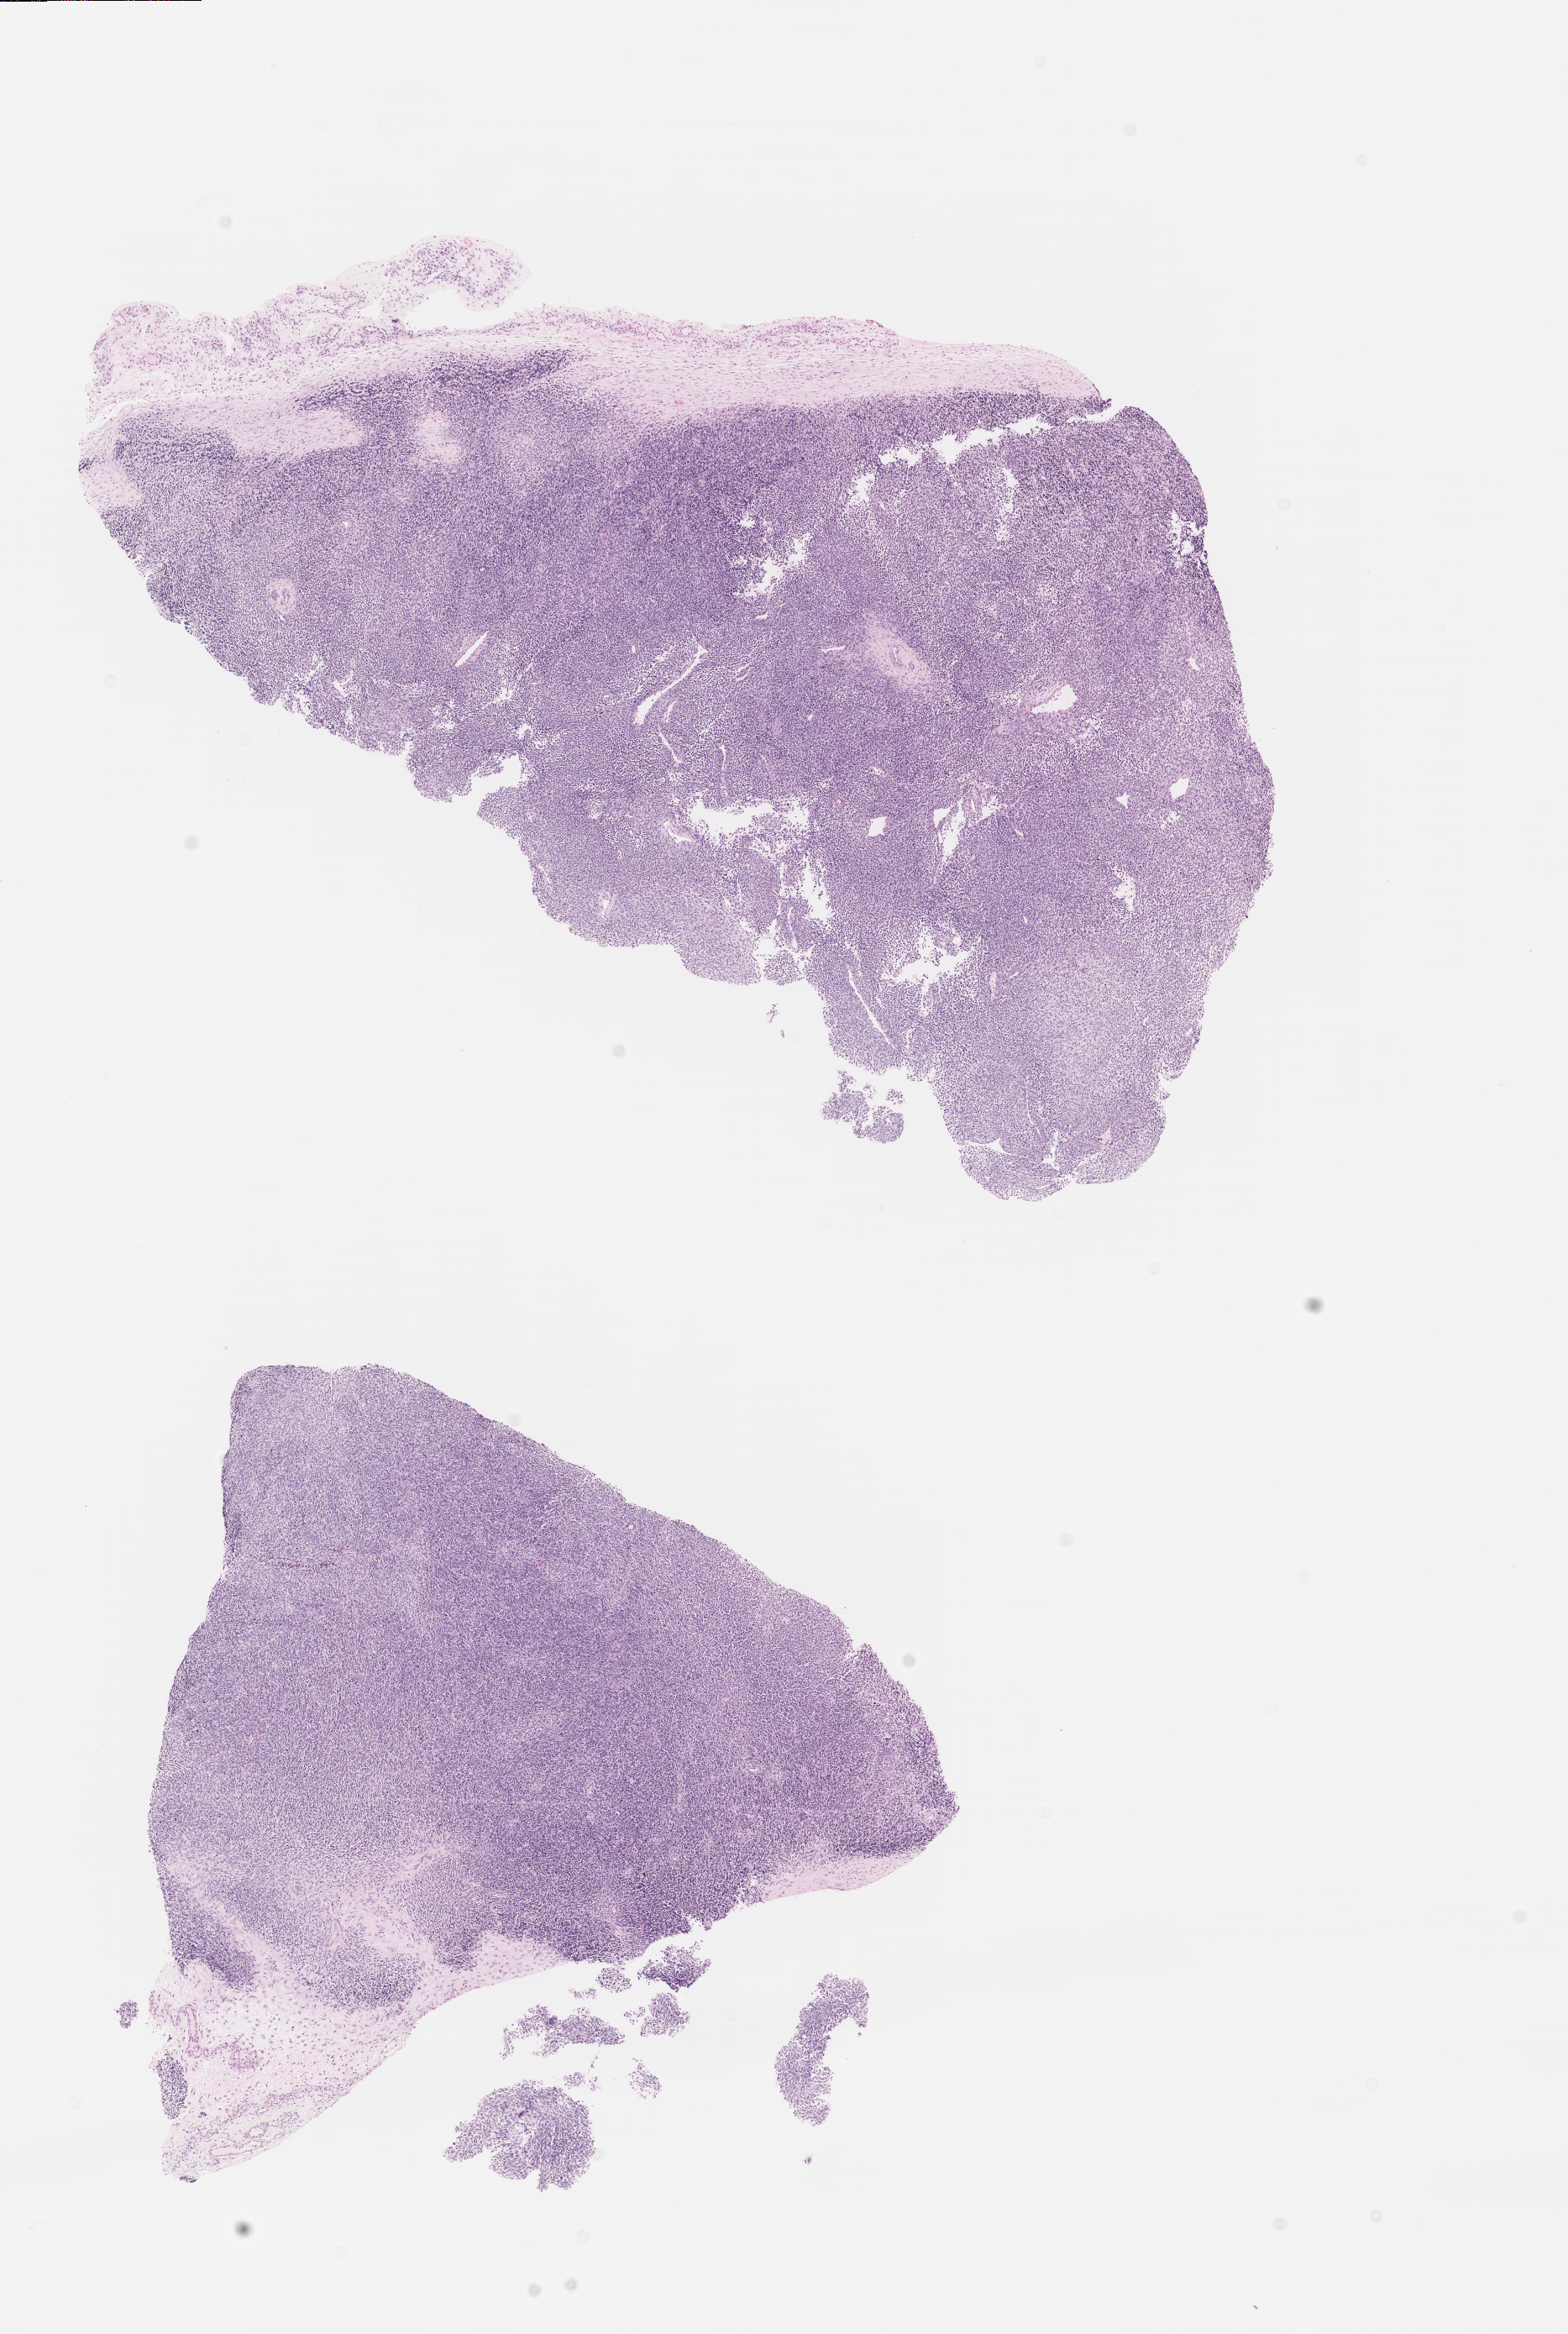
Whole-slide image, haematoxylin and eosin stain of tumor tissue — low-resolution overview of the scanned area, about 7.5 x 11.2 mm; formalin-fixed paraffin-embedded section; sample anatomic site: retroperitoneum. Patient: male, age 3.4 years at diagnosis.
Diagnosis: rhabdomyosarcoma; histological classification: embryonal rhabdomyosarcoma.